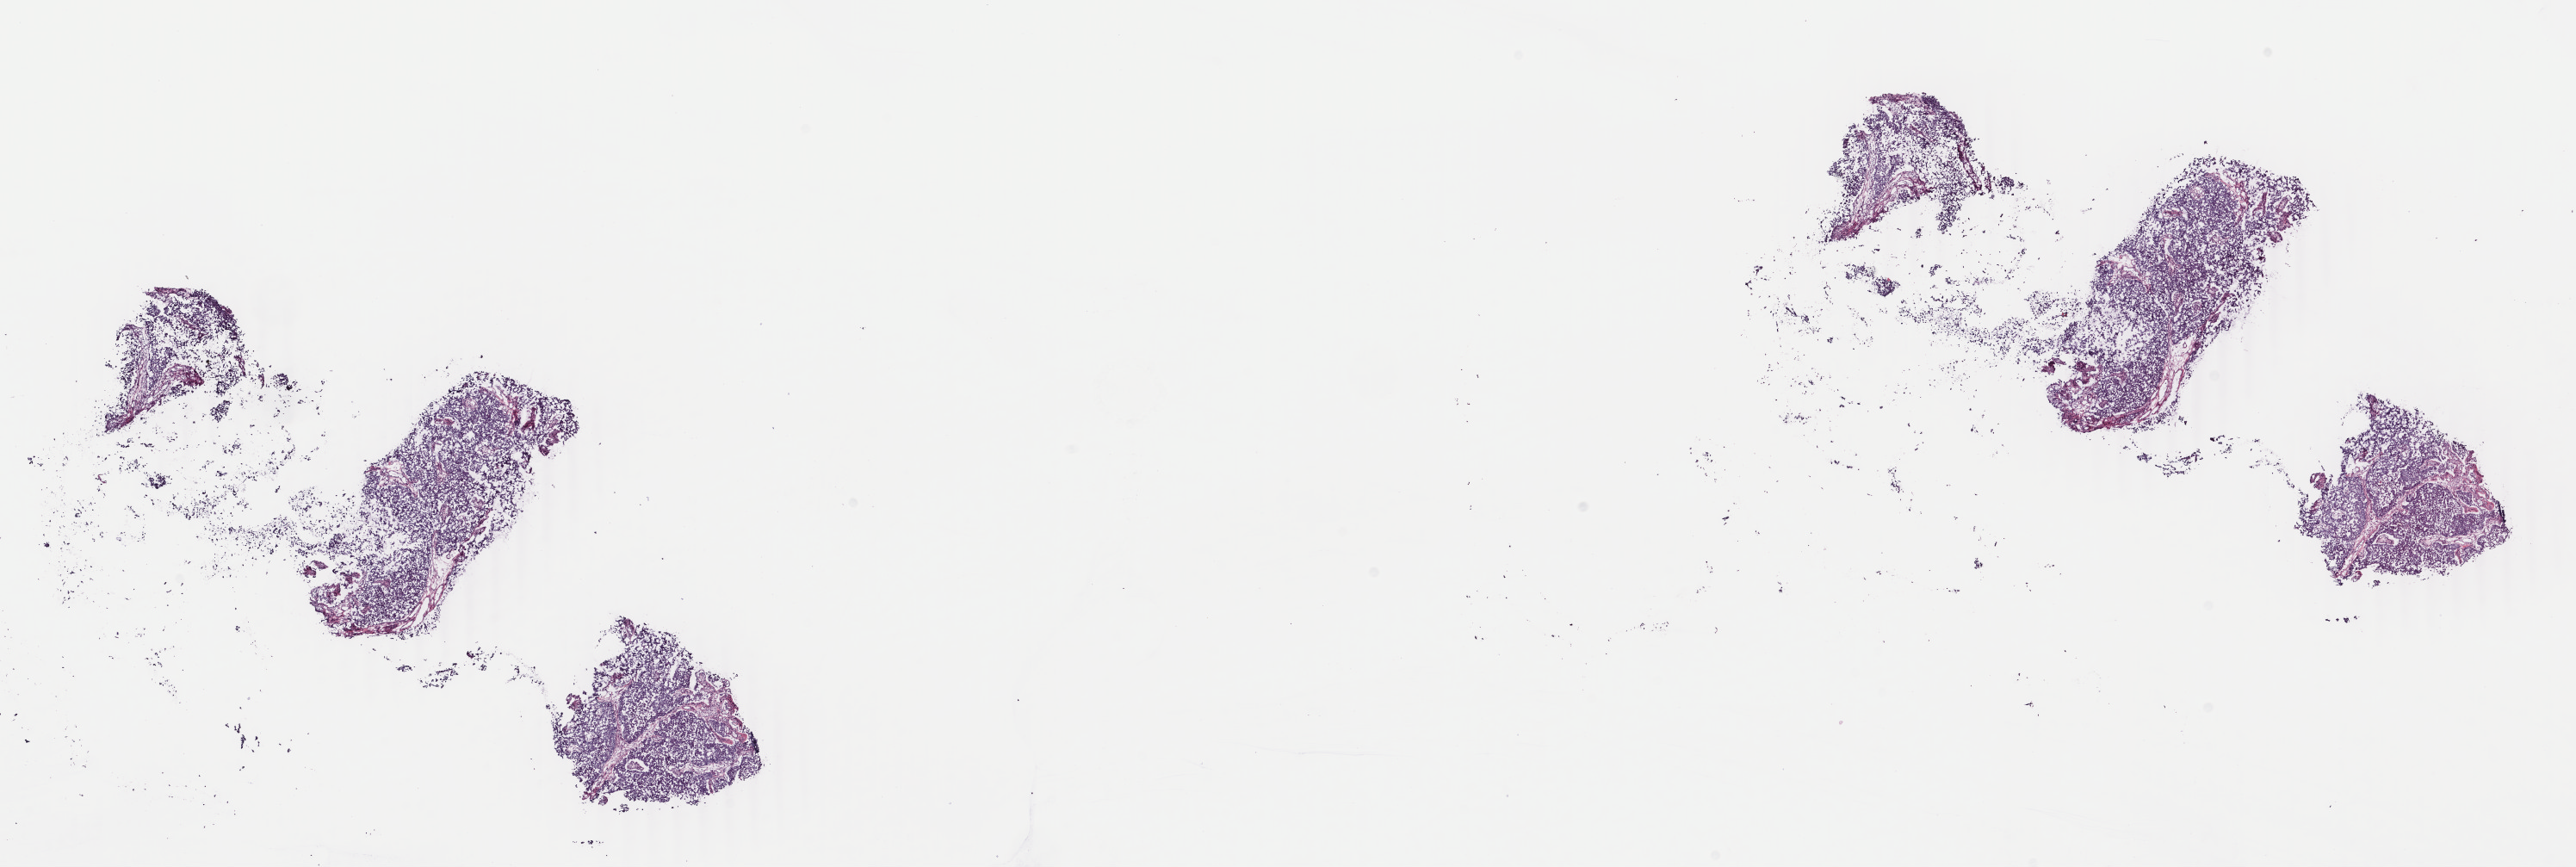
H&E-stained whole-slide image, shown as a low-resolution overview of the whole scanned area (about 23.8 x 8.0 mm), frozen section from the top of the tissue portion, sample: primary tumour, bladder. Male, age 67 years at initial diagnosis. Histologic grade: high grade. Slide review estimates, as recorded: tumour cells 100%, tumour nuclei 80%, normal cells 0%, stromal cells 0%, necrosis 0%. Inflammatory infiltration, as recorded: lymphocyte infiltration 1%, monocyte infiltration 0%, neutrophil infiltration 0%.
* diagnosis: Transitional cell carcinoma (anterior wall of bladder)
* AJCC pathologic stage: II